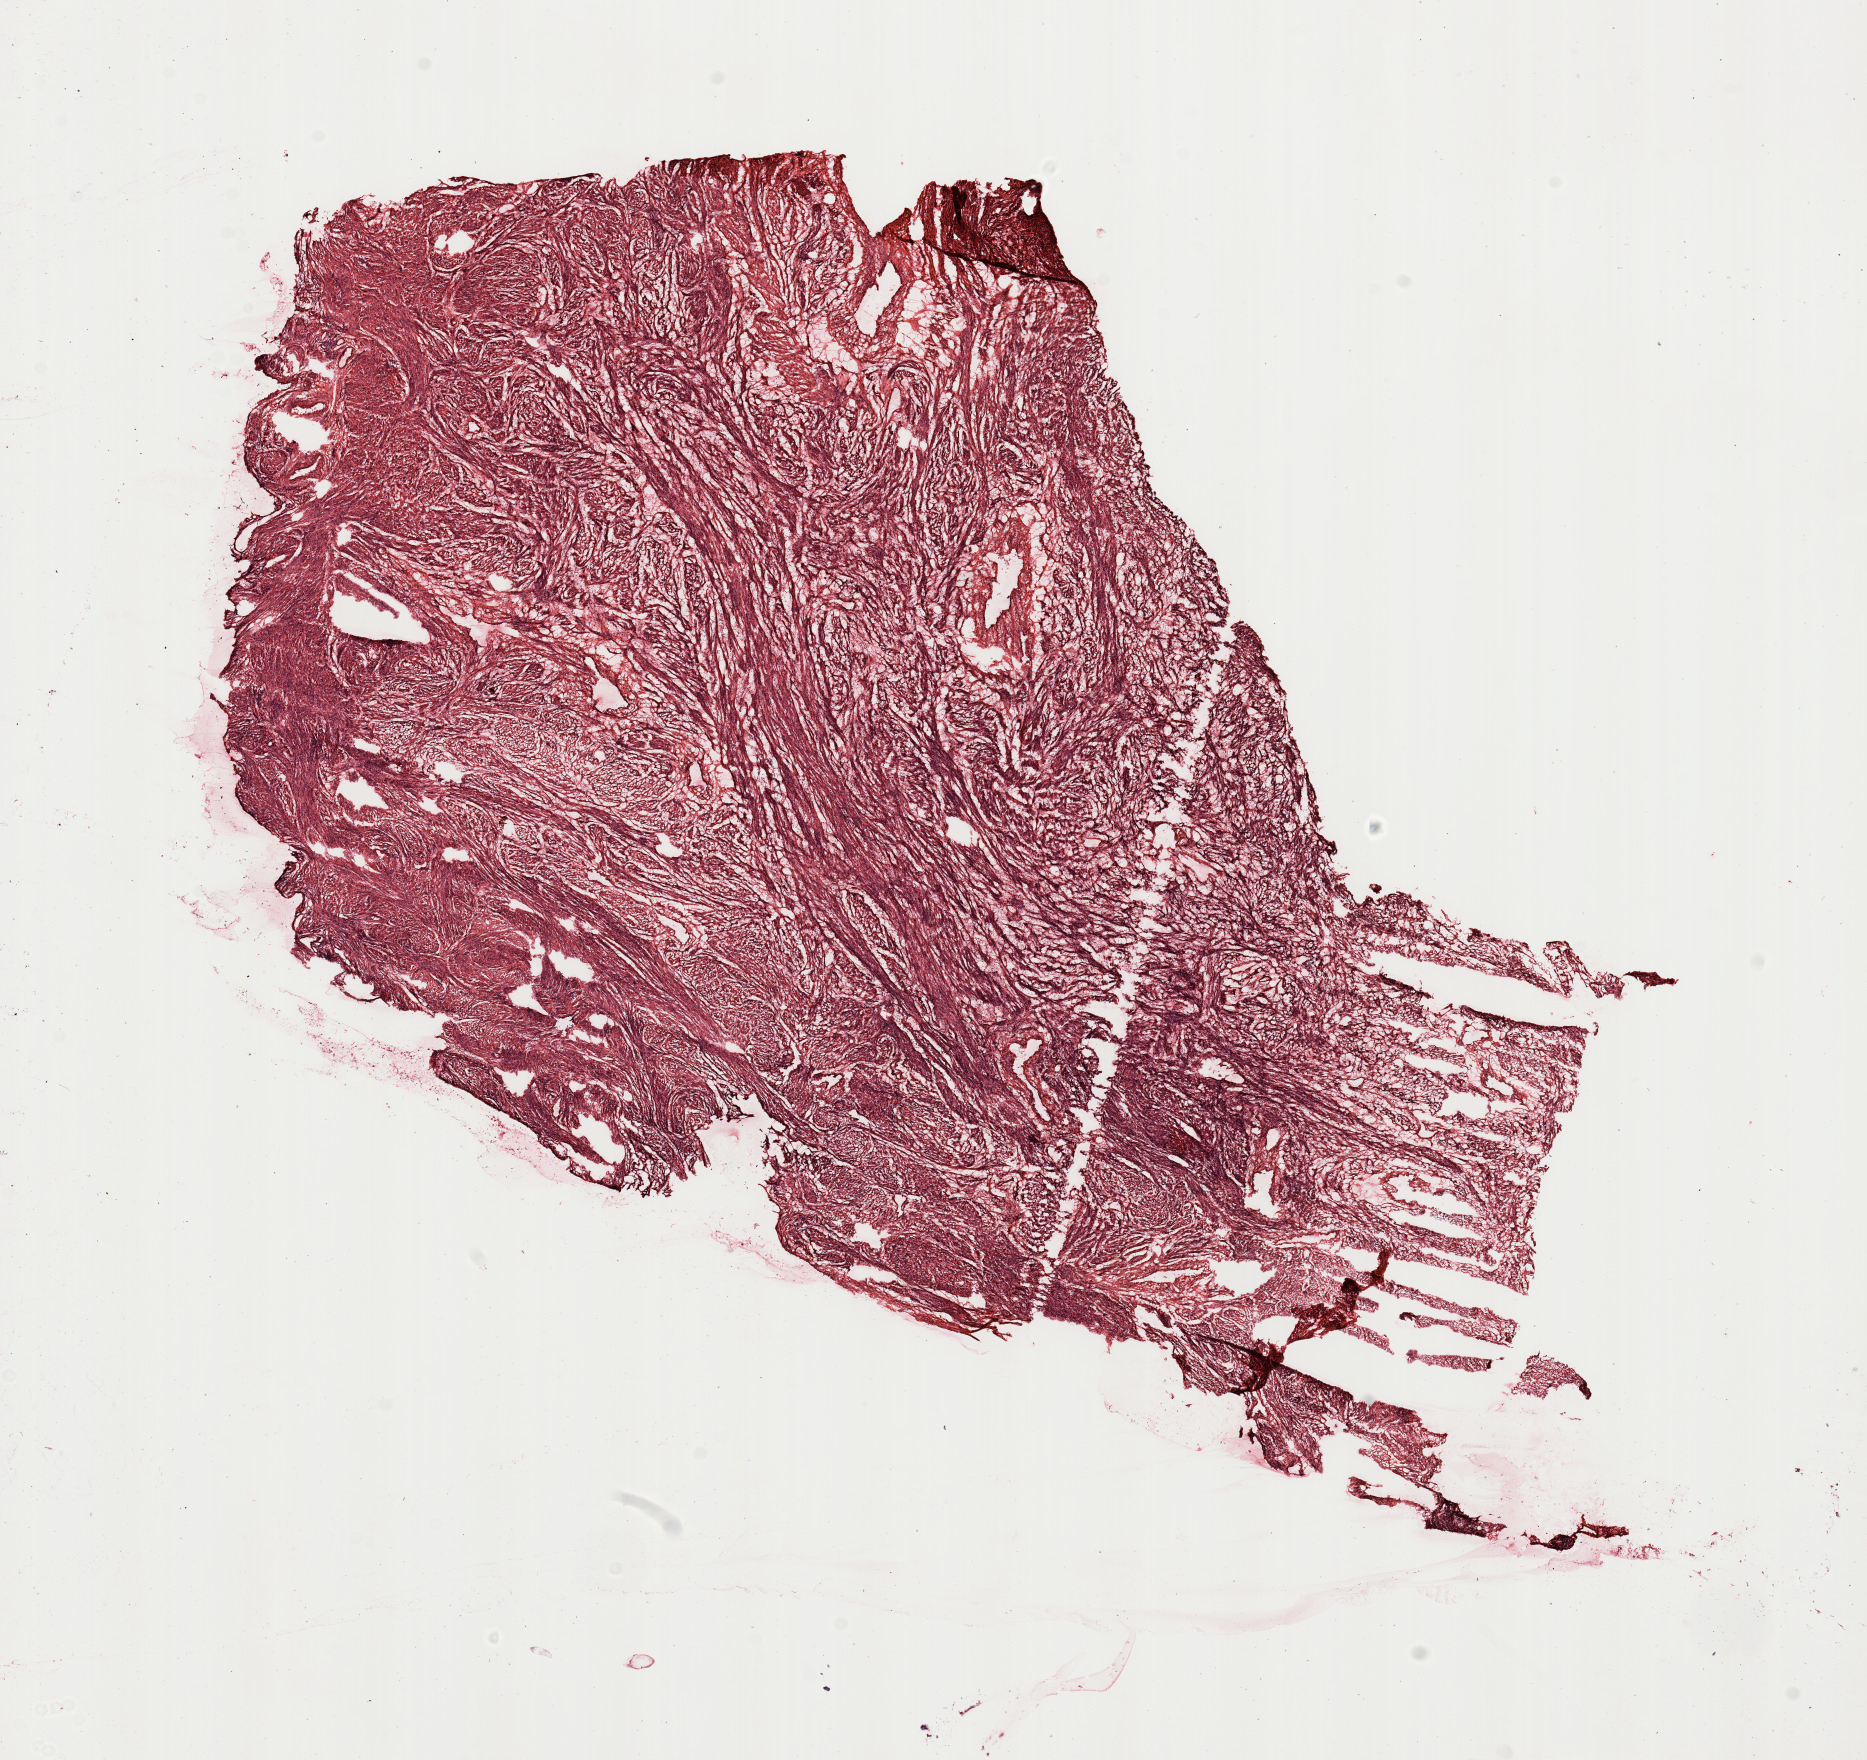
Whole-slide histology image, H&E-stained, a low-resolution overview of the entire scanned area, about 14.8 x 13.9 mm (acquisition: 20x scan), normal (non-tumour) tissue sample, uterus. 57-year-old female patient.
This section: normal (non-tumour) tissue from the same patient. Patient diagnosis: Endometrioid adenocarcinoma, NOS.